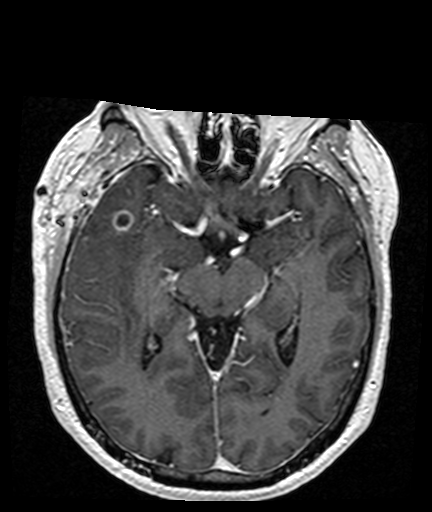
Brain MRI from a brain-tumour surgery series, one axial slice. Slice 98 of 176 in the series (ordered by position). T1-weighted post-contrast. 1 mm slice thickness. 432 × 512 image matrix, field of view 194 × 230 mm. From the clinical record (not read from this slice): histopathology: Glioblastoma; WHO grade: 4; IDH mutation: no.
Annotated regions visible in this slice (manually delineated by an expert):
- tumour: bounding box <112,212,134,231> (left, top, right, bottom; pixels)